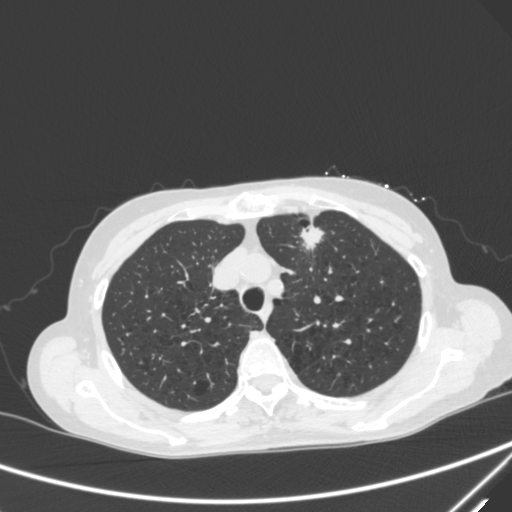
Chest CT, one axial slice. Position 233 of 300 along the scan axis. 120 kVp. Lung window (W 1500 / L -600 HU). 1 mm slice thickness. 512 × 512 image matrix, field of view 350 × 350 mm. Female patient, age 71 years. Case-level facts recorded for this patient, not image findings: clinical TNM (as recorded): T1c N0 M0; histopathological grade: G2-3.
Outlined on this slice (rectangle marked by the reading radiologist):
- lung tumour (recorded histology: adenocarcinoma): bounding box (x1, y1, x2, y2) in pixels: (297, 218, 331, 263)